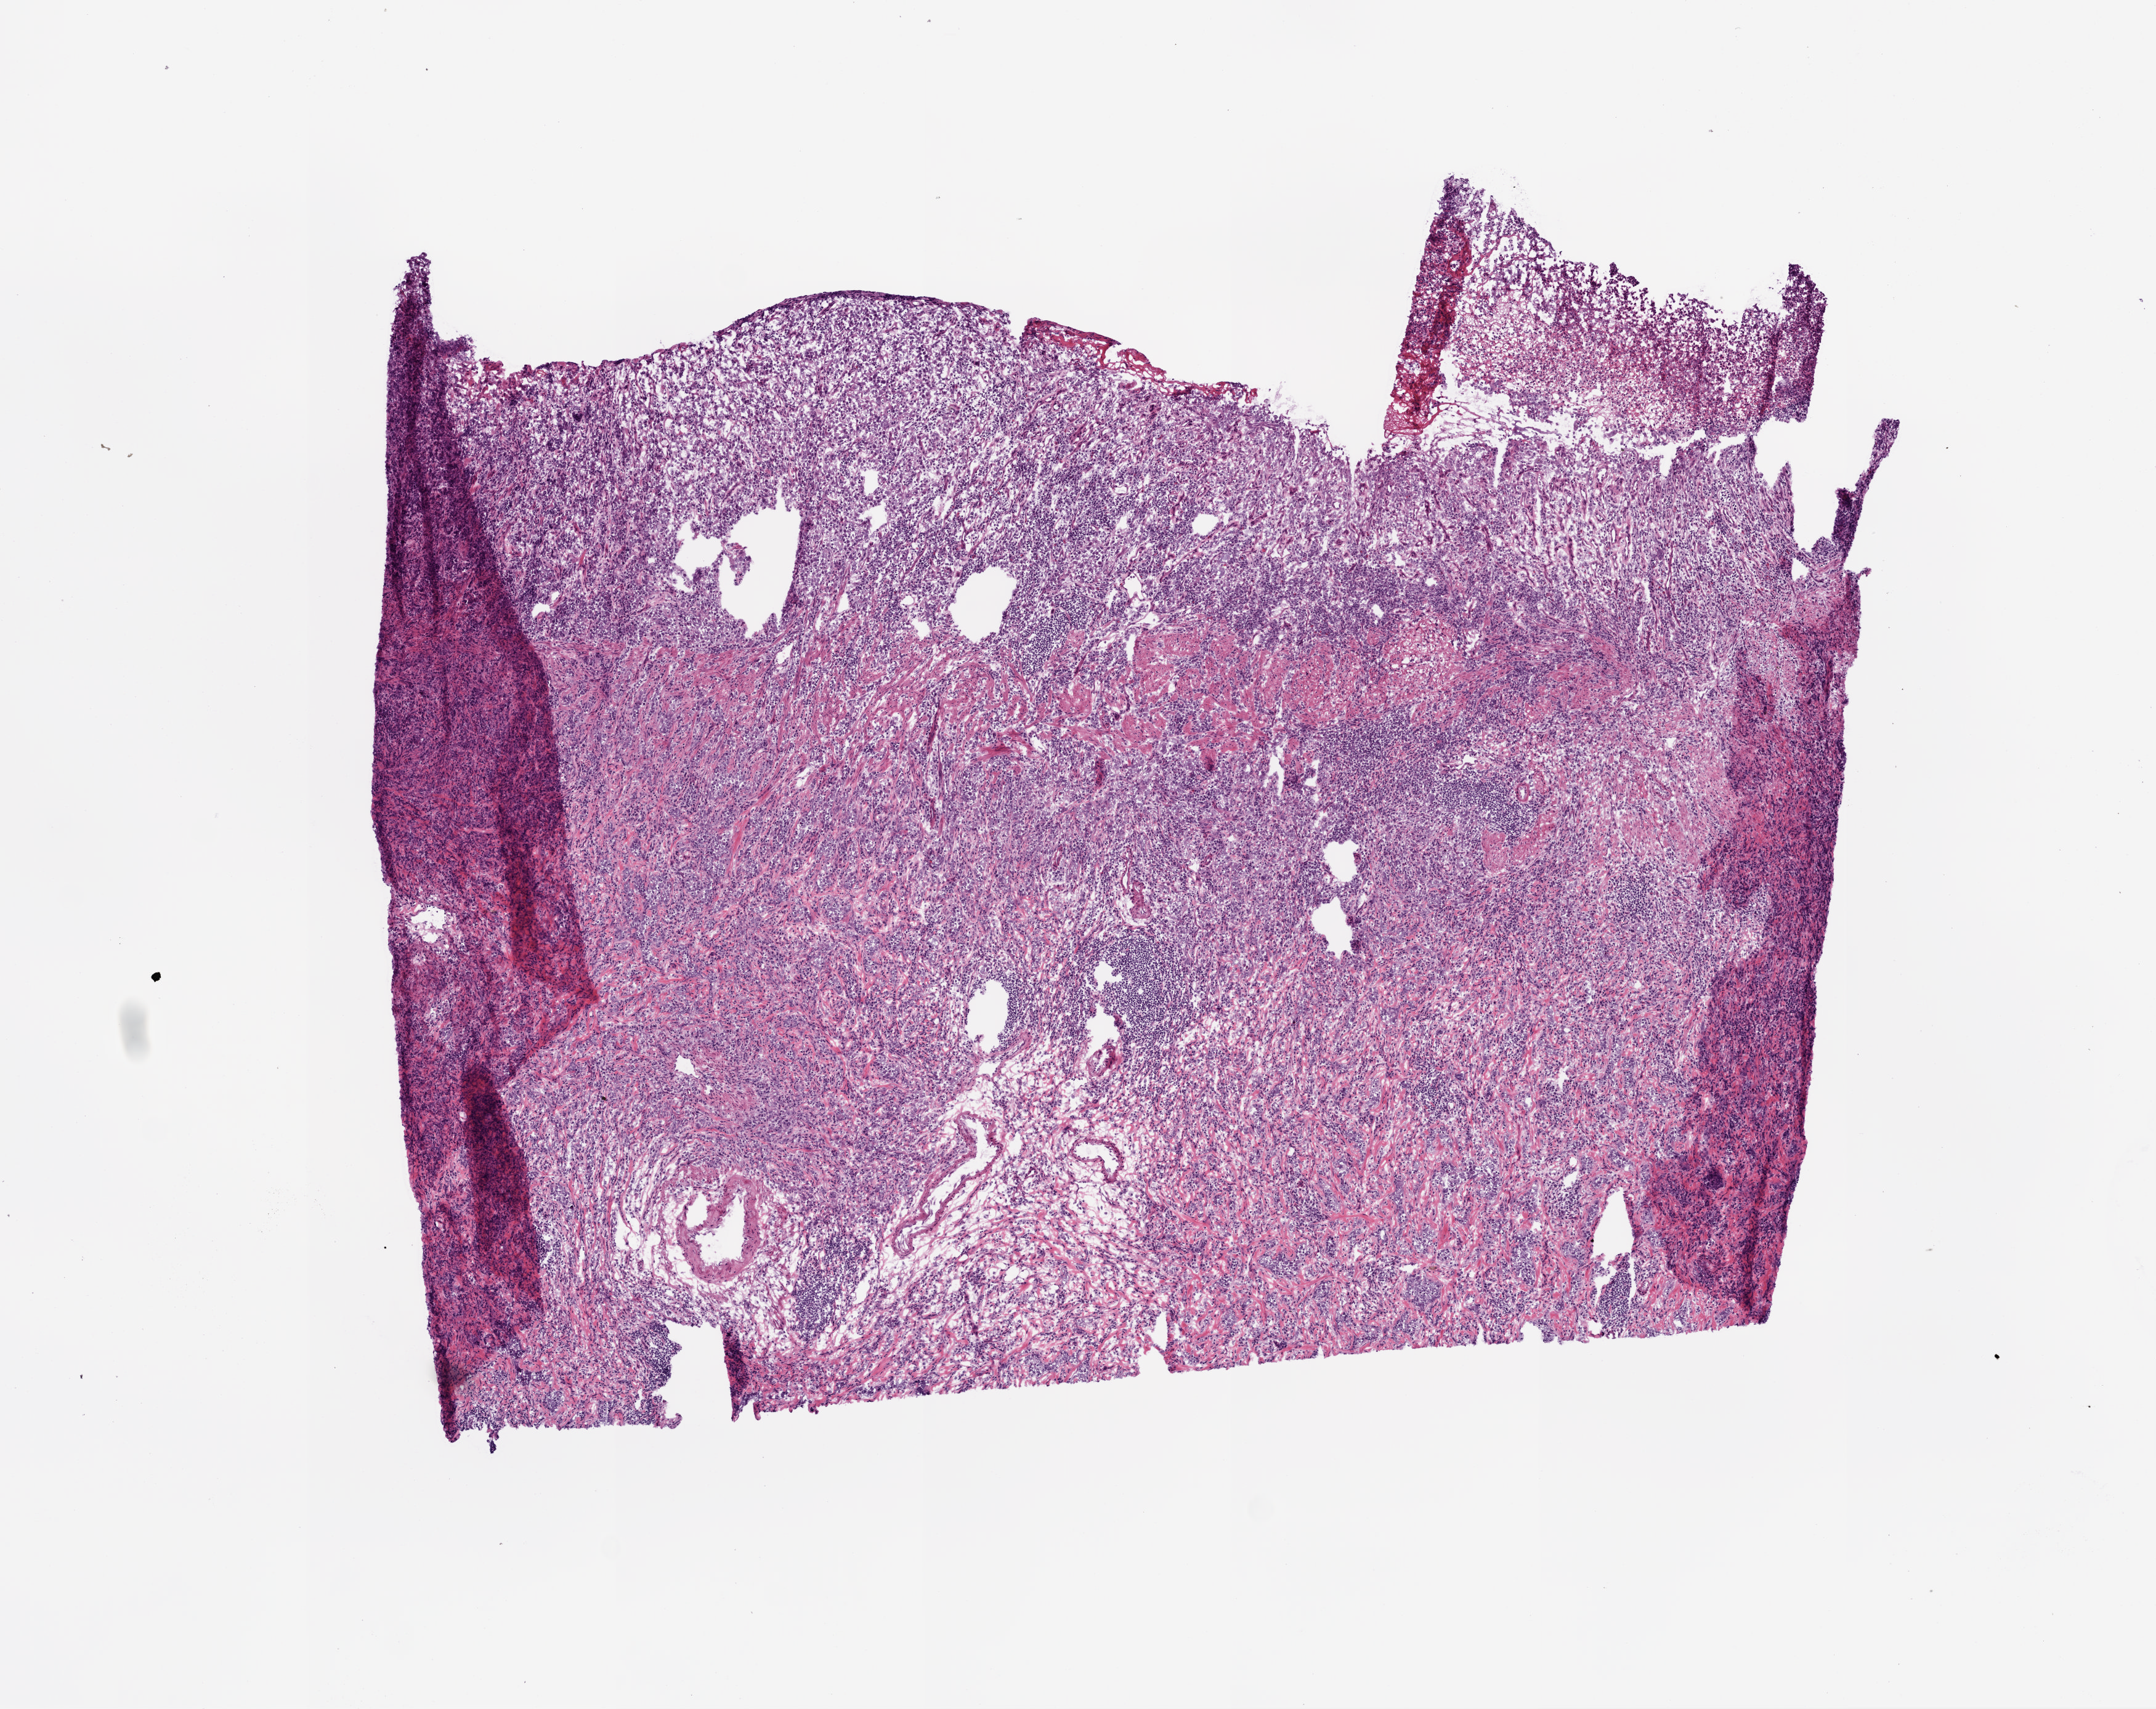
Whole-slide histology image, H&E-stained, whole scanned area (about 7.0 x 5.6 mm) shown as a low-resolution overview; frozen section; stomach, primary tumour sample. Female patient; age at initial diagnosis 67 years.
Histologic diagnosis: Adenocarcinoma, intestinal type (body of stomach).